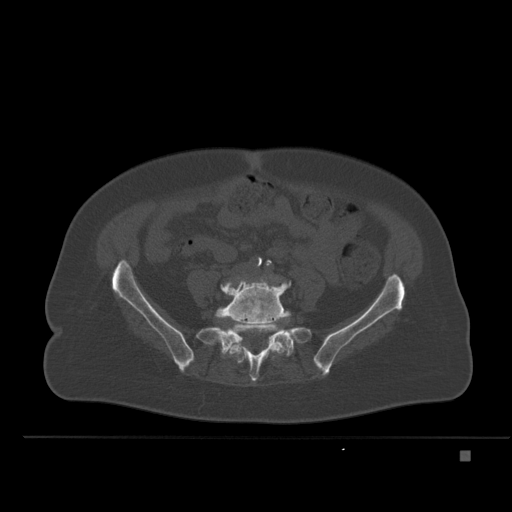
CT including the spine, one axial slice; position 156 of 477 along the scan axis; bone window (W 1800 / L 400 HU); 512 × 512 image matrix, field of view 422 × 422 mm. Female patient, age 74 years. From the clinical record (not read from this slice): primary cancer: colon.
Structures marked on this image (semi-automatic segmentation, software-assisted and operator-edited):
- L5 vertebra: box from (x=216, y=277) to (x=291, y=356) px